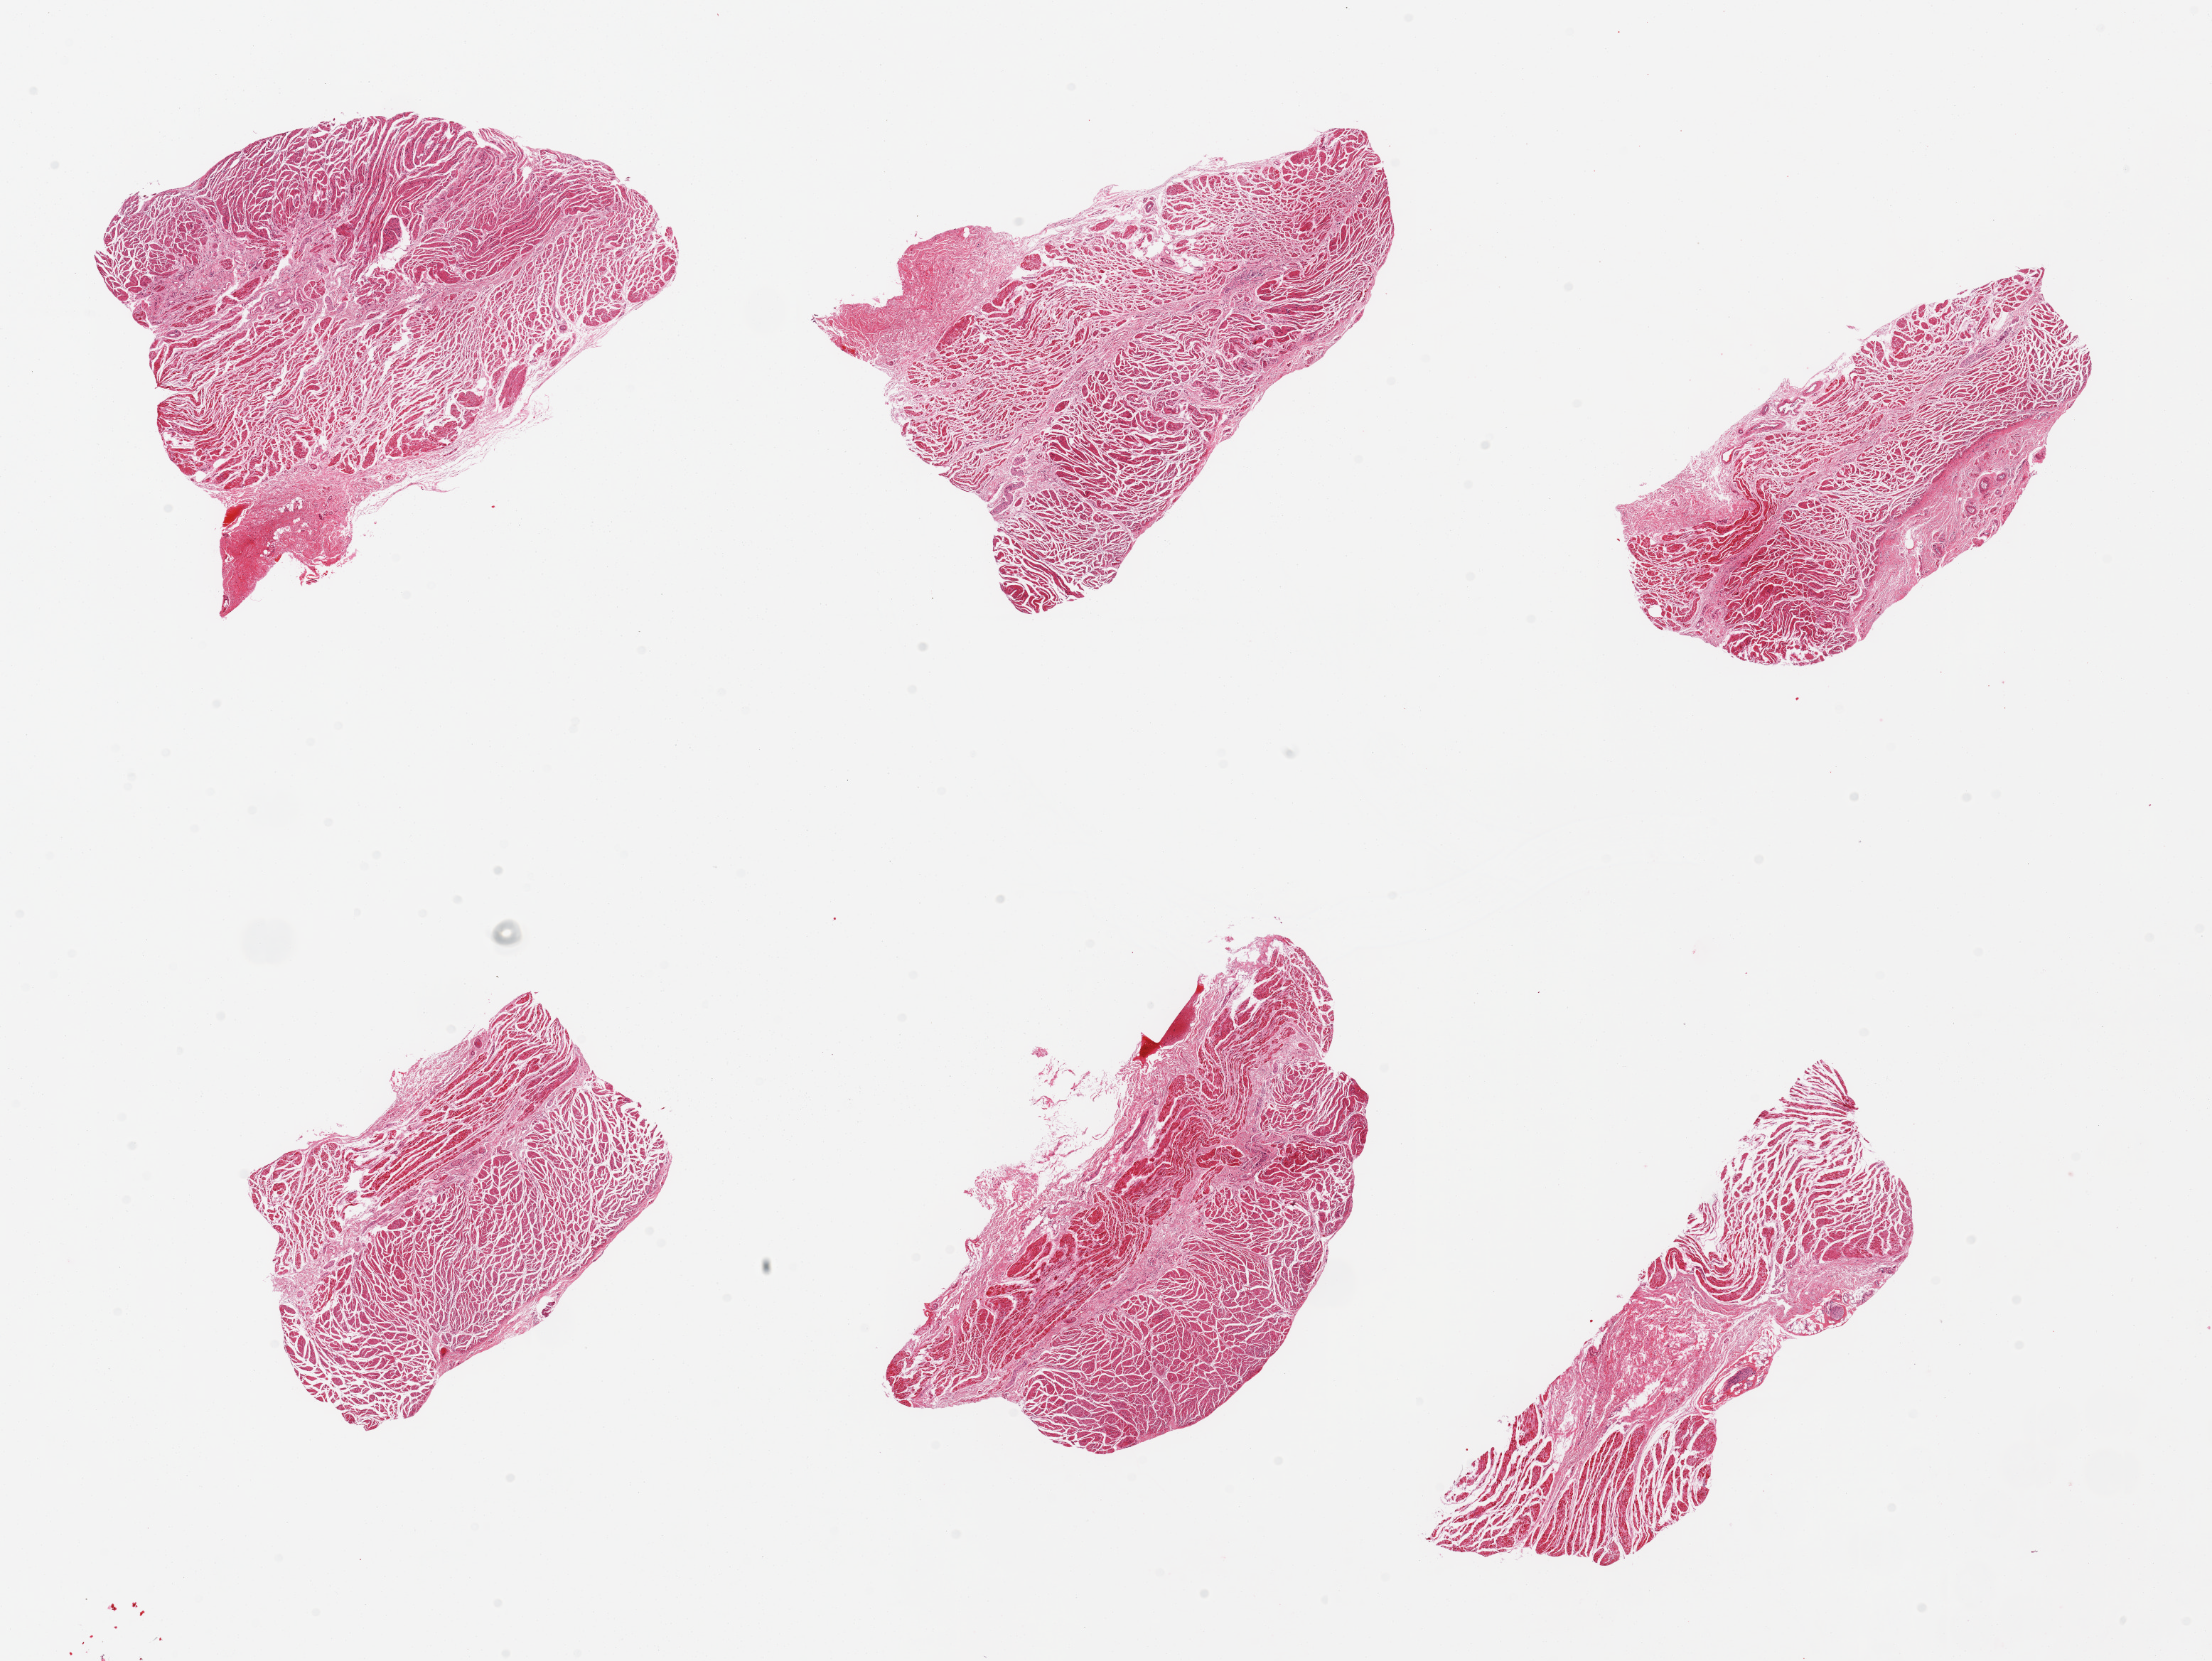
Whole-slide image, haematoxylin and eosin stain, shown as a low-resolution overview of the whole scanned area (about 24.6 x 18.5 mm), PAXgene-fixed paraffin-embedded (PFPE) section, section of esophageal muscle (target tissue), tissue donor sample. Male donor.
Pathologist's review note for this sample: 6 pieces, all muscularis, good specimens.